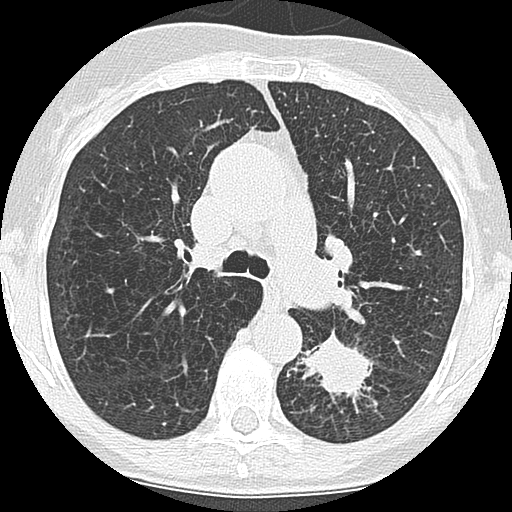
Low-dose screening chest CT, one axial slice; slice 115 of 171 in the series (ordered by position); 120 kVp; lung window (W 1500 / L -600 HU); 2.5 mm slice thickness; 512 × 512 image matrix, field of view 280 × 280 mm.
Structures marked on this image (expert manual segmentation):
- lesion 1 (tumor, lower lobe of left lung): bounding box <302,333,372,396> (left, top, right, bottom; pixels)